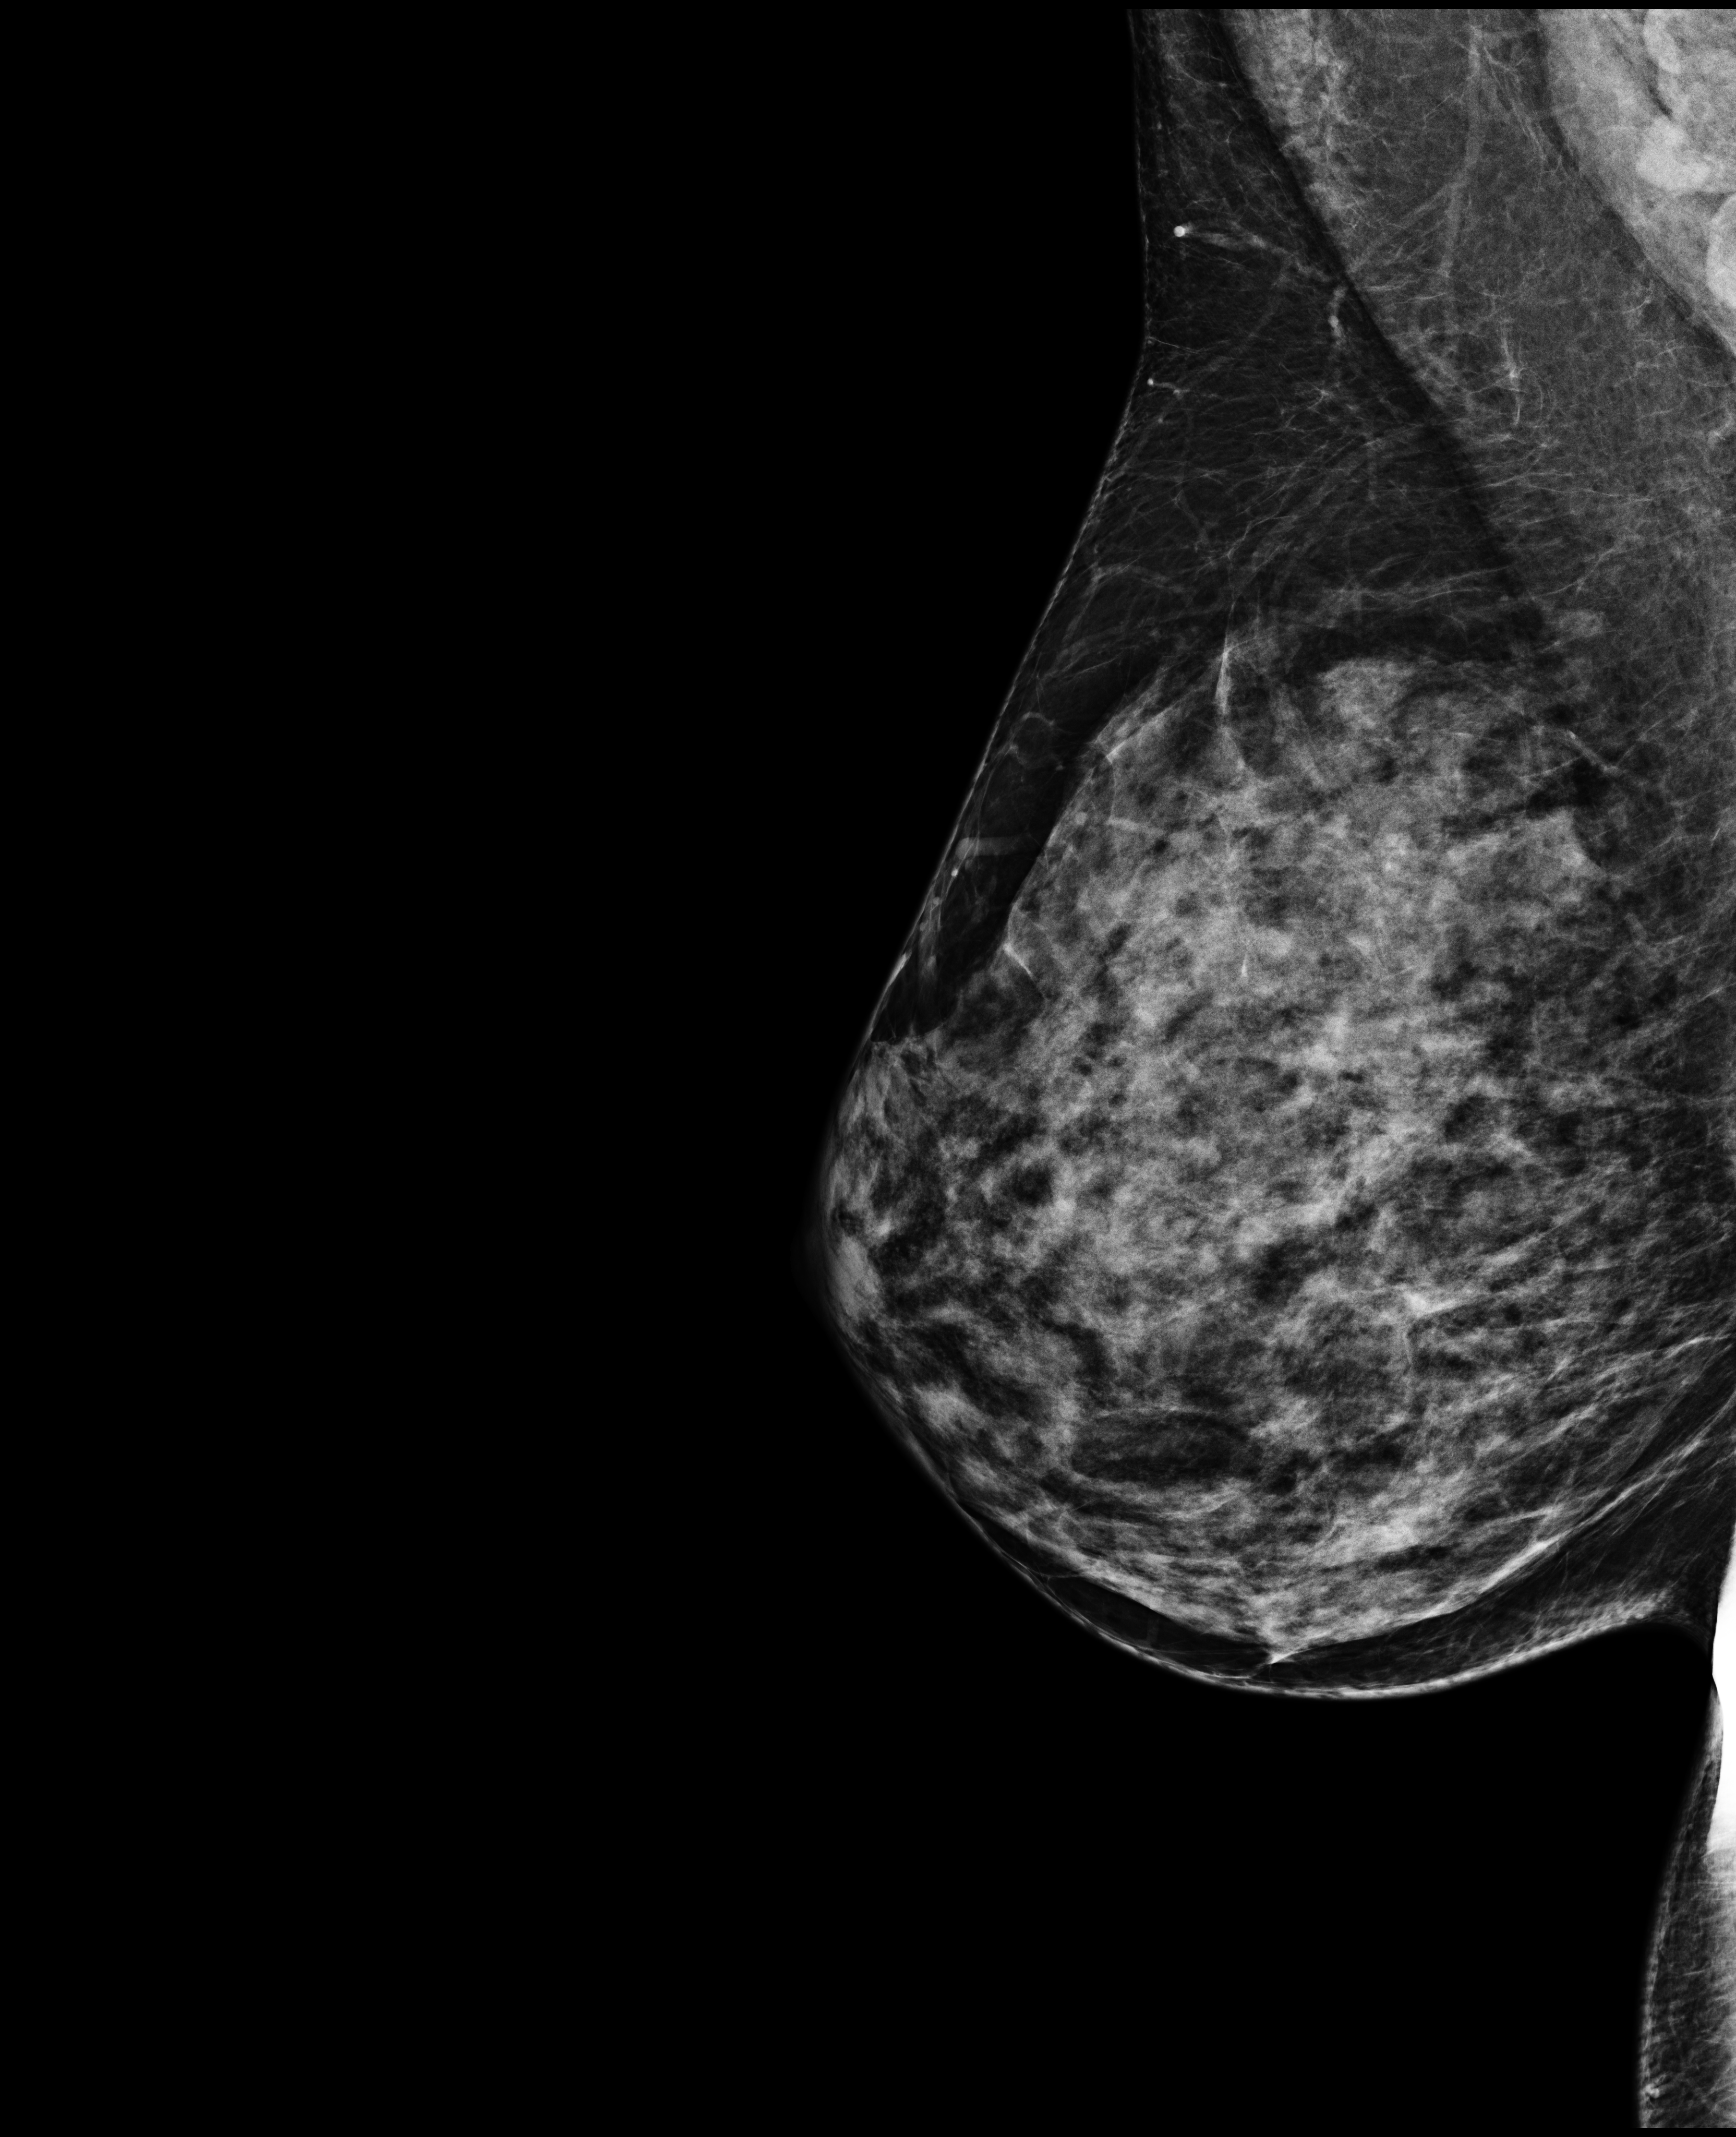
Annual screening mammography examination. Patient aged 43 years (female).
Image type: full-field digital mammogram. Breast: right. Projection: medio-lateral oblique projection.